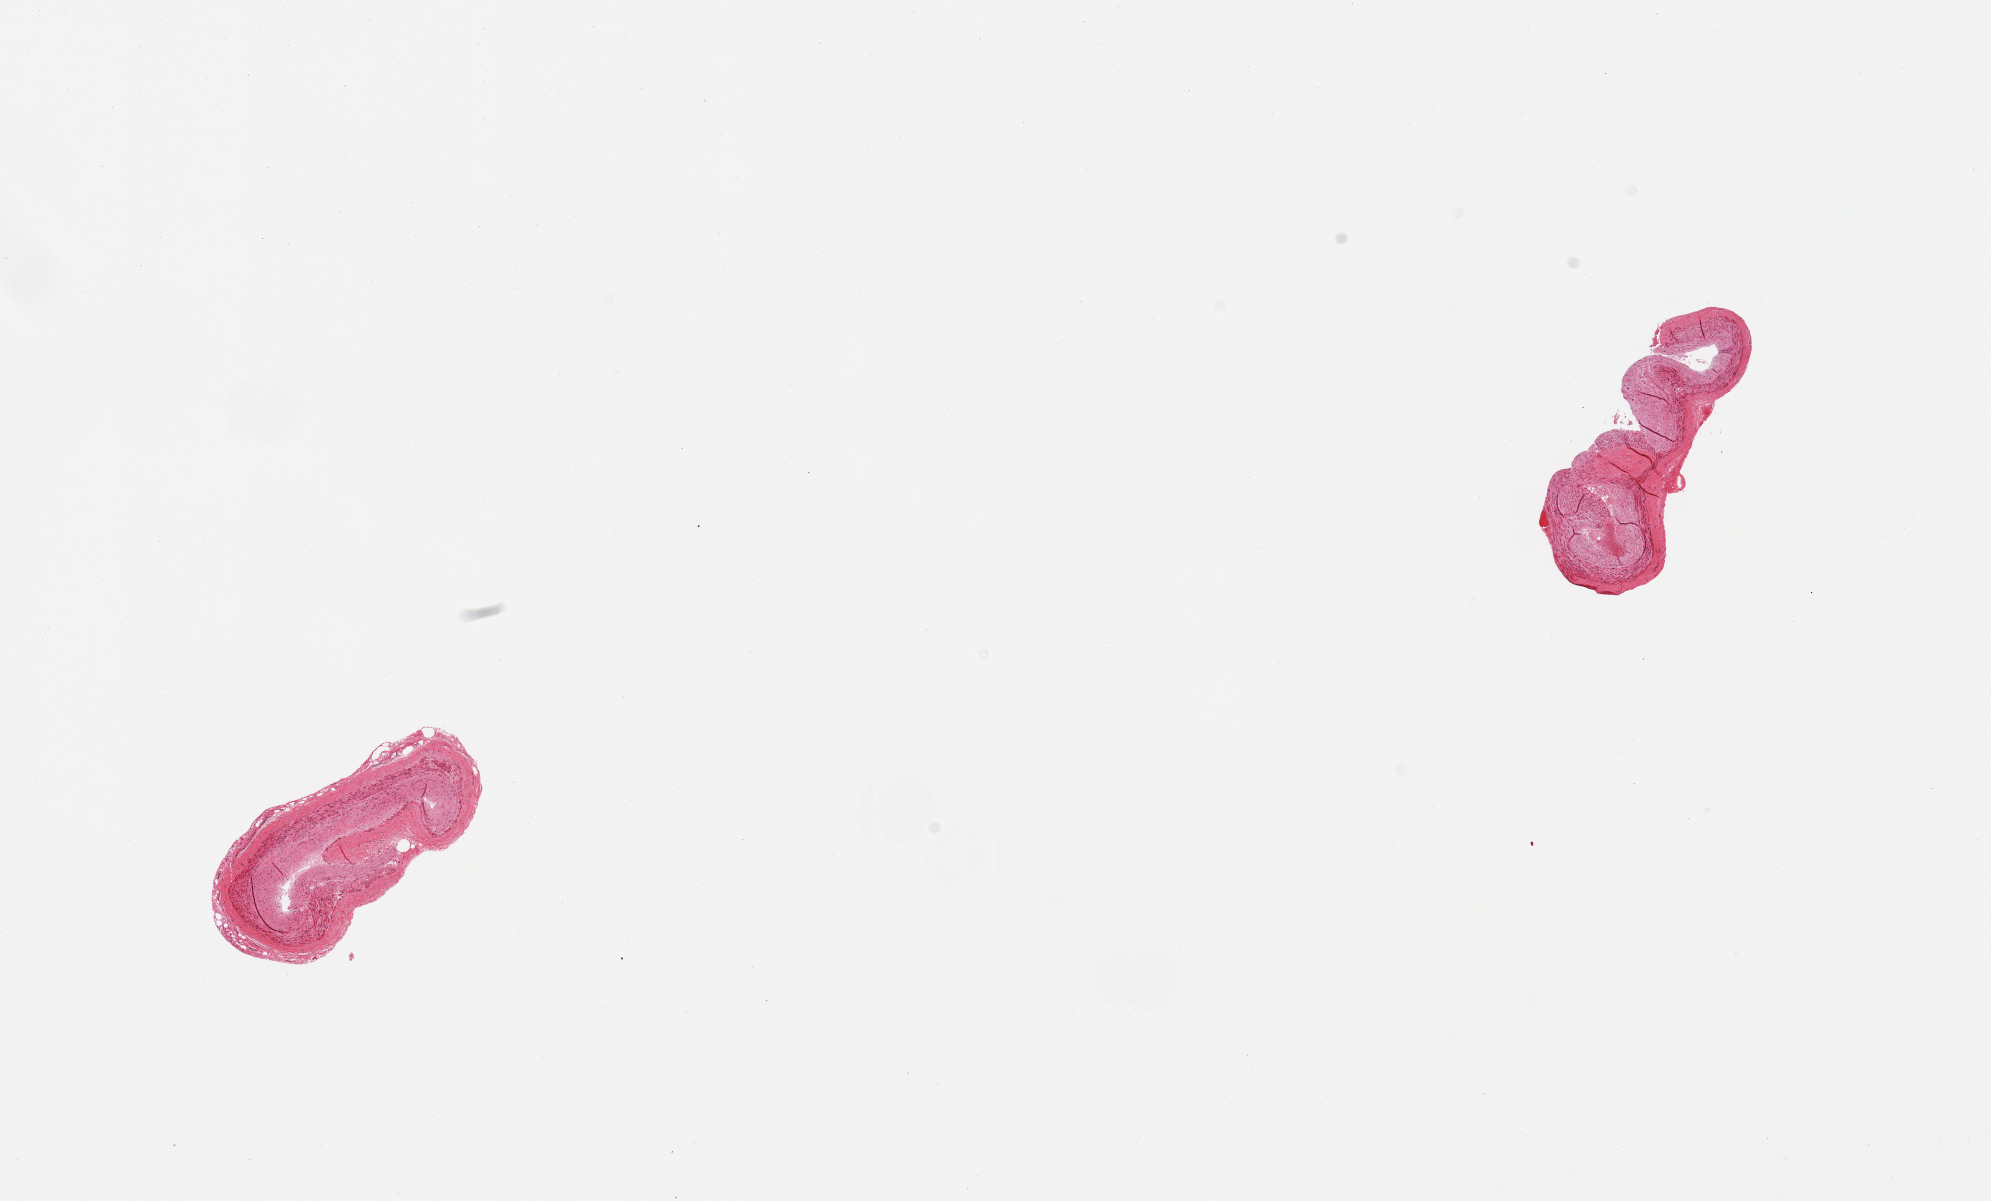
Whole-slide image, H&E stain, low-resolution overview of the scanned area, about 15.8 x 9.5 mm (from a 20x scan); PAXgene-fixed paraffin-embedded (PFPE) section; section of coronary artery (target tissue); tissue donor sample. Donor sex: male.
- reviewer comment on this tissue sample: 2 pieces; well trimmed